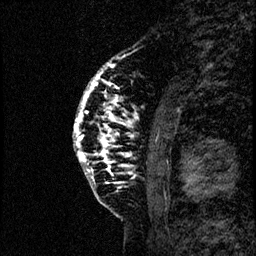
Breast MRI (dynamic contrast-enhanced), one sagittal slice; position 17 of 60 along the scan axis; dynamic contrast-enhanced study with each time point stored as its own series, time point 2 of 4 at this slice position (early post-contrast, ordered by acquisition time); 1.5 T; TE 4.2 ms, TR 17.6 ms; 2 mm slice thickness; 256 × 256 image matrix, field of view 200 × 200 mm. Female patient, age 40 years. Case-level facts recorded for this patient, not image findings: setting: breast cancer imaged before/during neoadjuvant chemotherapy; receptor status: HER2-positive.
Outlined on this slice (semi-automatically segmented with operator editing):
- analysis volume of interest (the breast-tissue region the enhancement analysis was run in; not a lesion): bounding box <70,55,183,206> (left, top, right, bottom; pixels)
- tumour enhancement mask (voxels above the 100 % enhancement threshold inside the analysis volume of interest): <73,62,134,175>